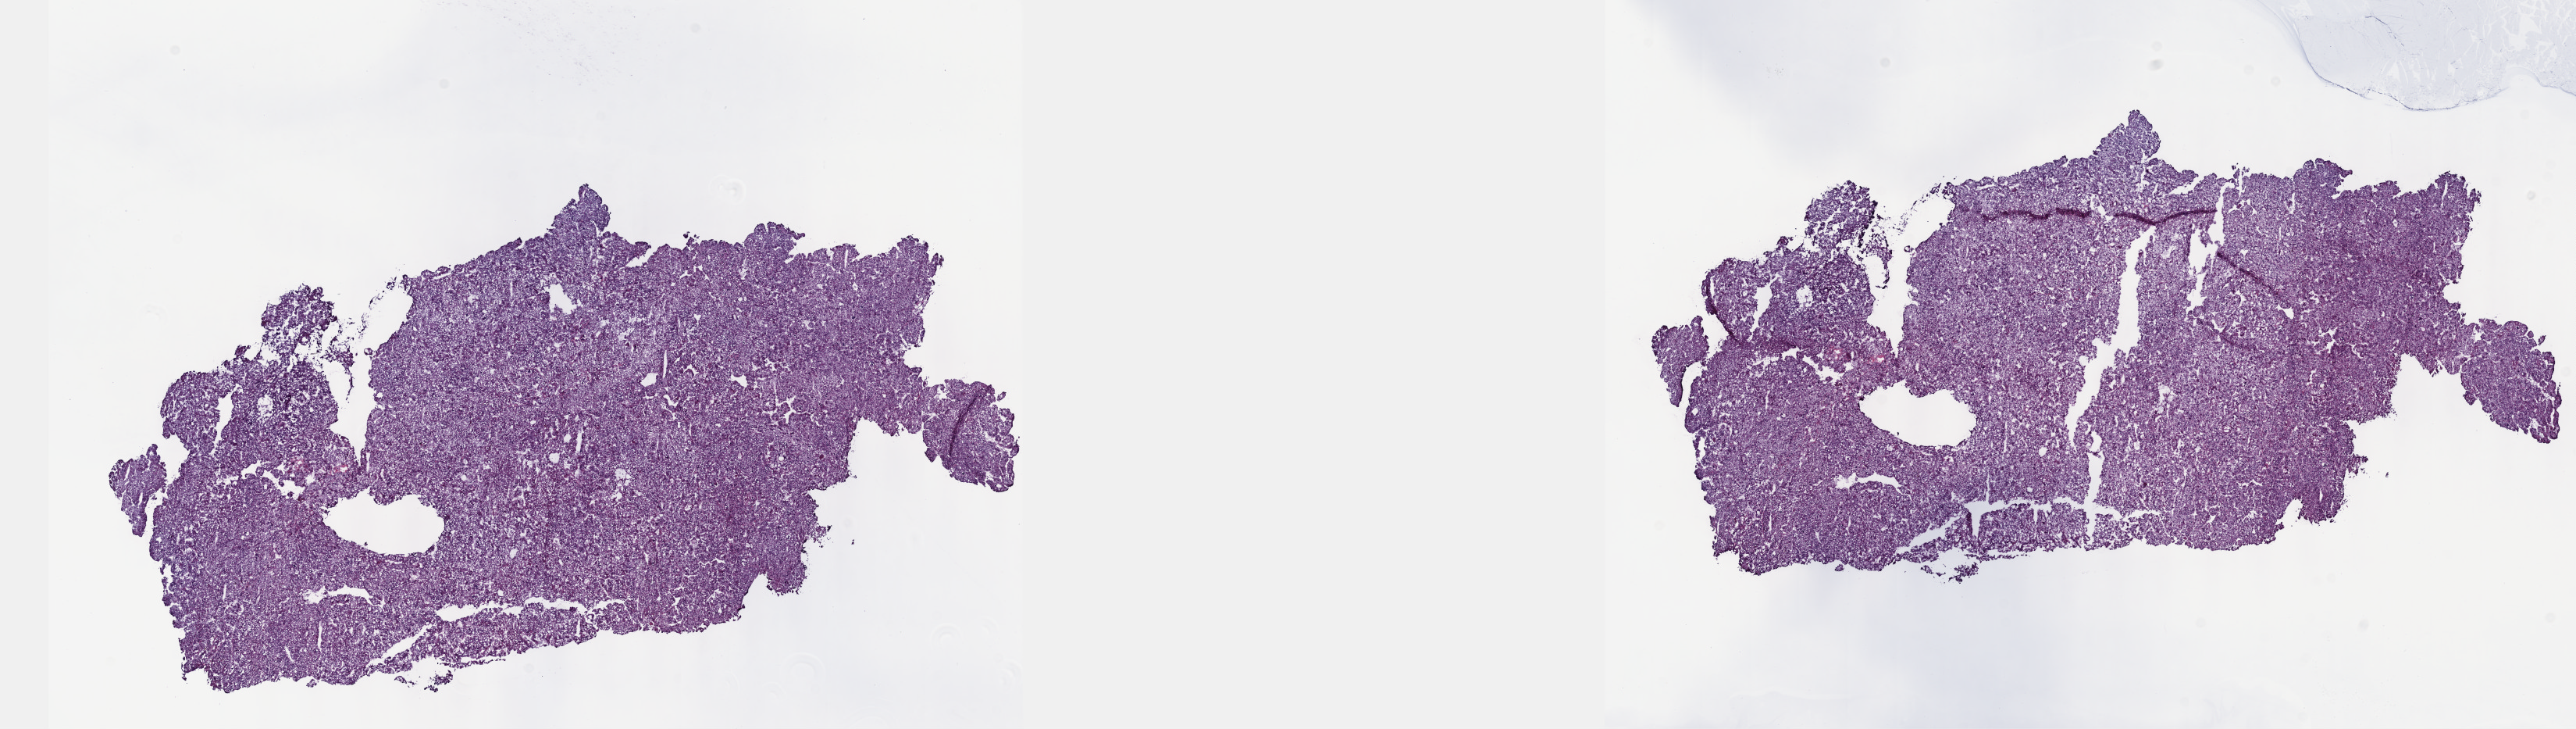
Digitized H&E tissue section (whole slide), a low-resolution overview of the entire scanned area, about 26.7 x 7.5 mm; frozen section from the top of the tissue portion; primary tumour sample from the liver. Male patient; age at initial diagnosis 51 years. Histologic grade: G3 (poorly differentiated). Pathologist review of this section (percent, as recorded): tumour cells 85%, tumour nuclei 85%, normal cells 0%, stromal cells 15%, necrosis 0%. Inflammatory infiltration, as recorded: lymphocyte infiltration 3%, monocyte infiltration 1%, neutrophil infiltration 1%.
AJCC pathologic stage: IIIC. Diagnosis: Hepatocellular carcinoma, NOS.